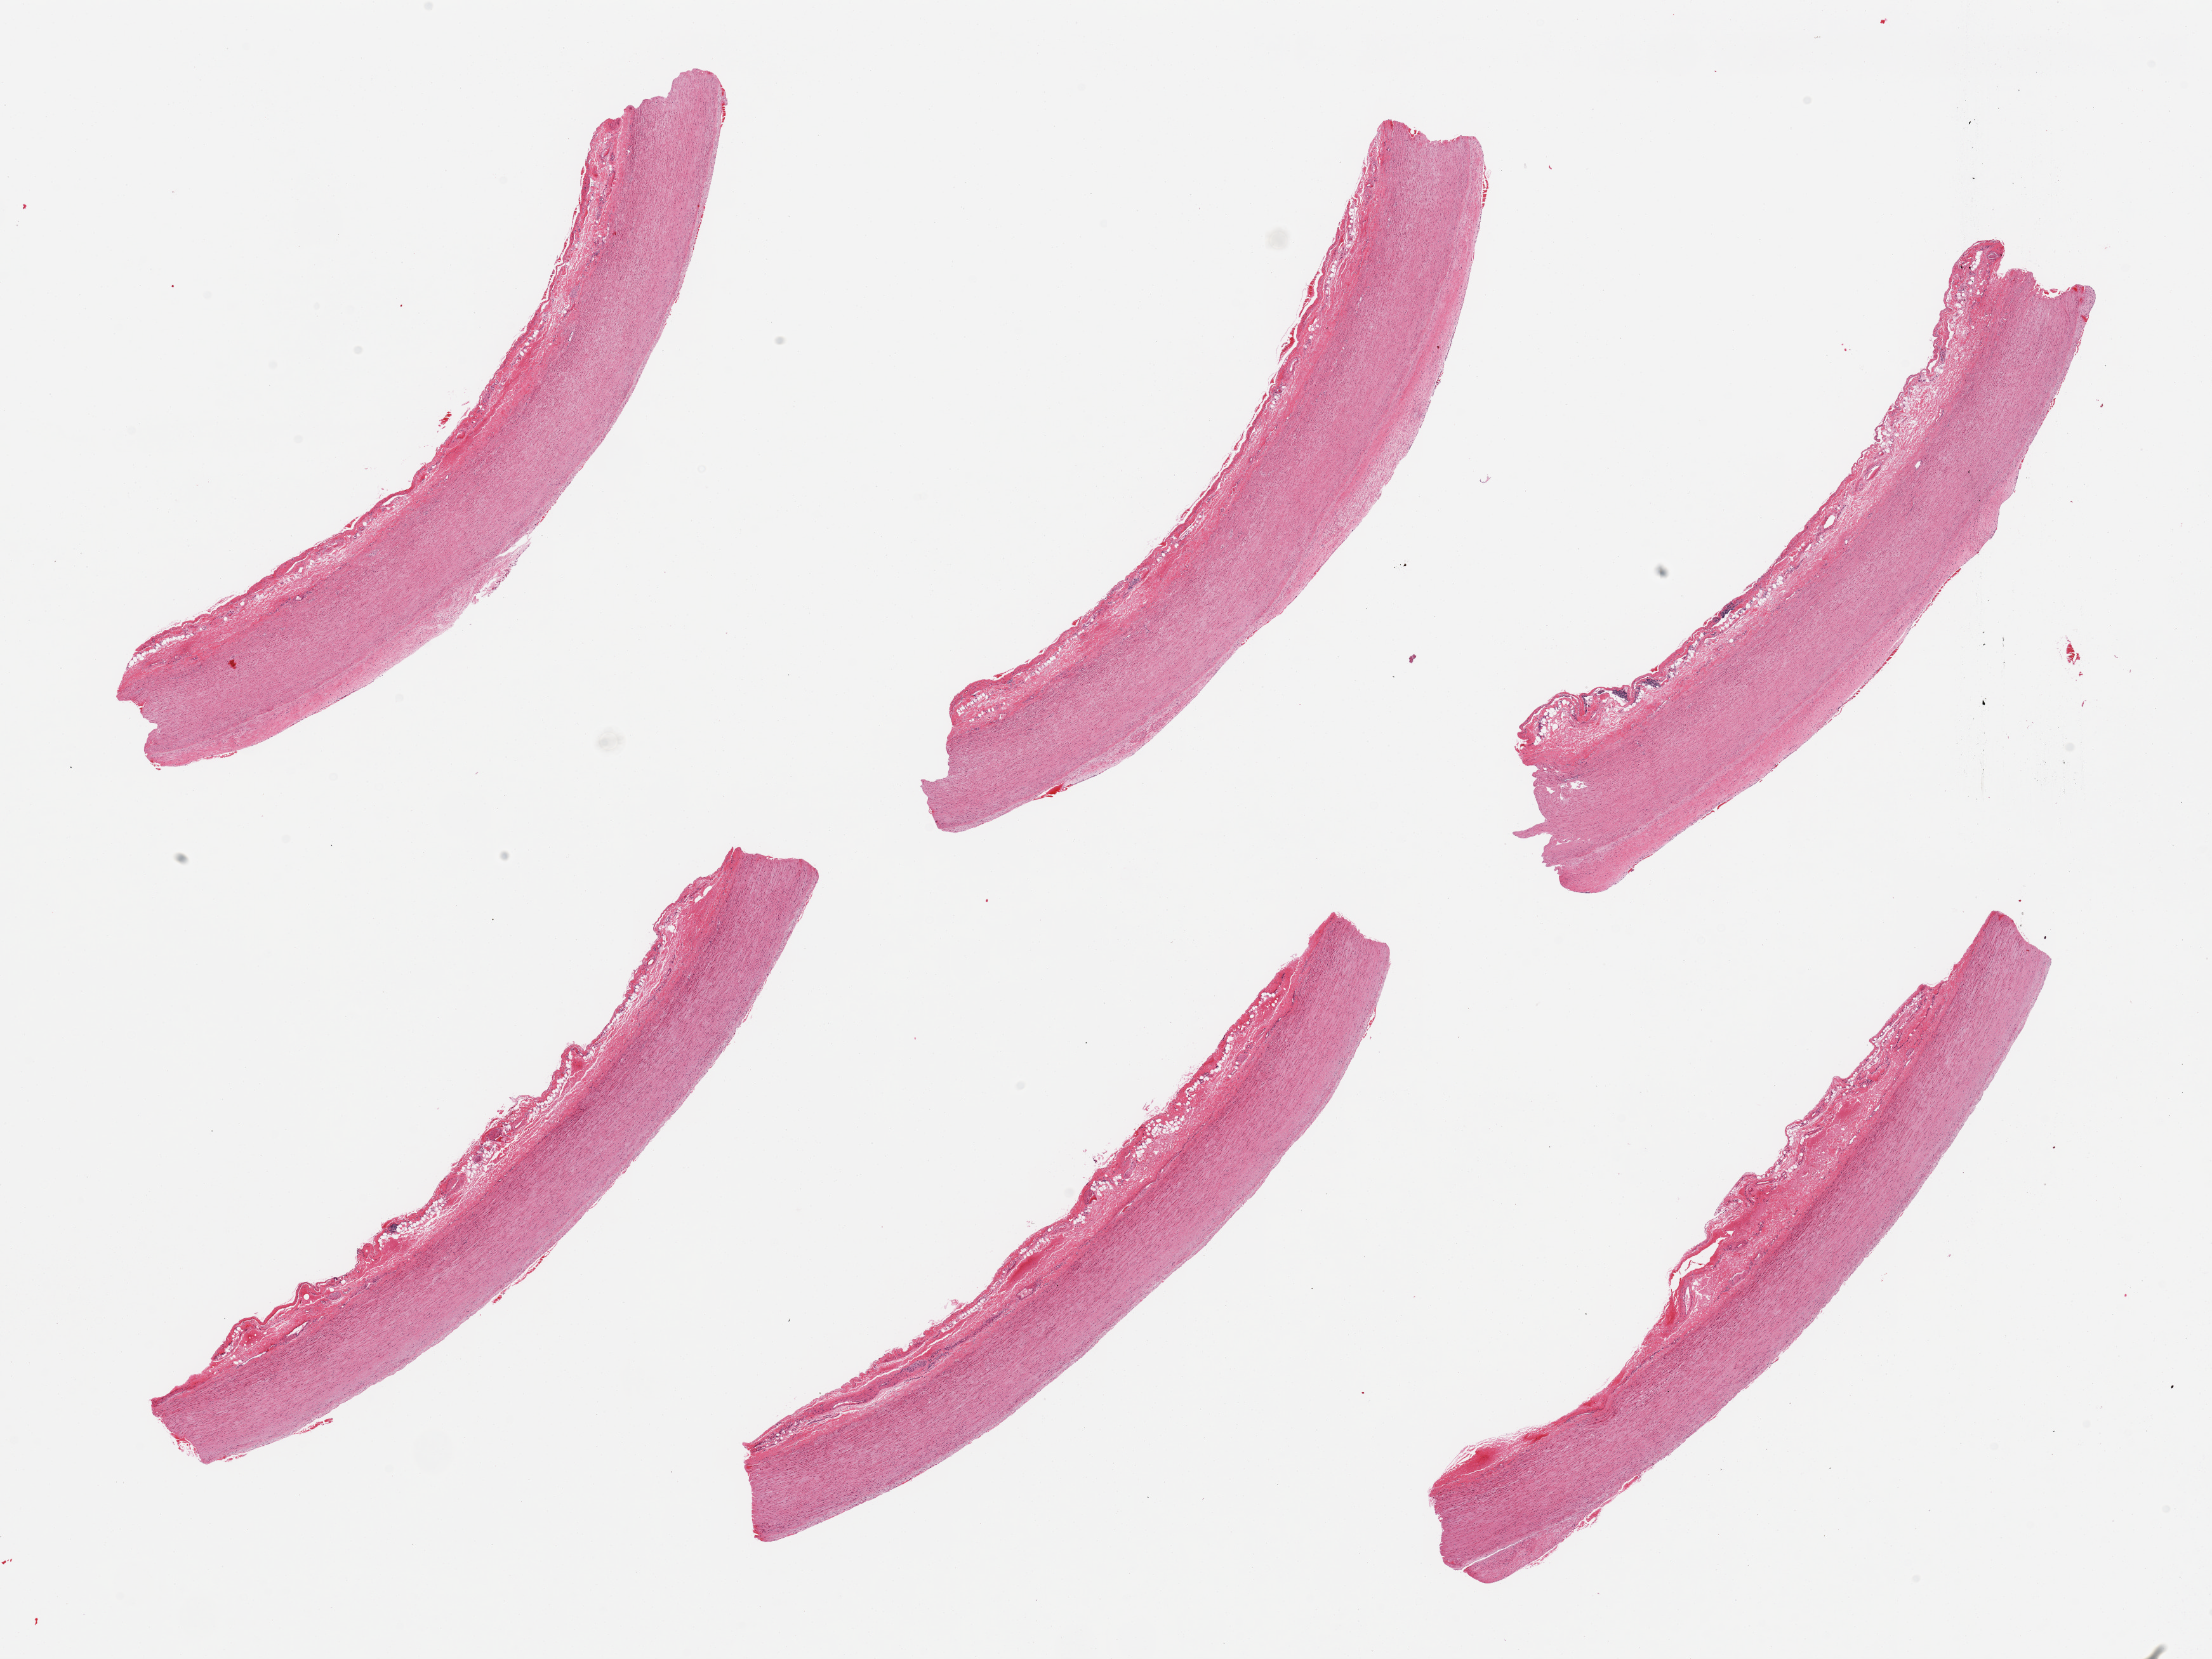
Whole-slide image, H&E stain, a low-resolution overview of the entire scanned area, about 27.6 x 20.7 mm (slide scanned at 20x). PAXgene-fixed, paraffin-embedded tissue. Sampled site (target tissue): aorta. Tissue donor sample.
- review note (as recorded): 6 pieces, adherent fat serosa up to ~0.5mm